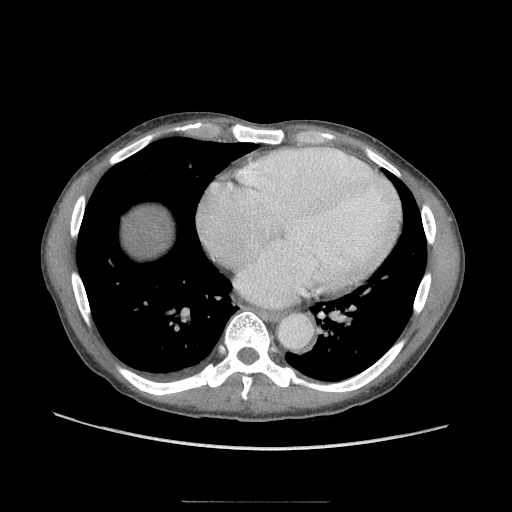
Contrast-enhanced abdominal CT (liver protocol), one axial slice; position 101 of 103 along the scan axis; reconstruction kernel STANDARD; 120 kVp; soft-tissue window (W 400 / L 40 HU); 512 × 512 image matrix, field of view 380 × 380 mm. From the clinical record (not read from this slice): diagnosis: hepatocellular carcinoma (patient treated with transarterial chemoembolisation; whether this scan precedes or follows treatment is not stated here); TNM stage (as recorded): Stage-IIIA; Child-Pugh class: A; tumour differentiation: moderately differentiated.
Annotated regions visible in this slice (semi-automatic segmentation, software-assisted and operator-edited):
- liver parenchyma outside the tumour (the mass and vessels are separate outlines, so this box may not span the whole liver): box from (x=134, y=218) to (x=158, y=240) px